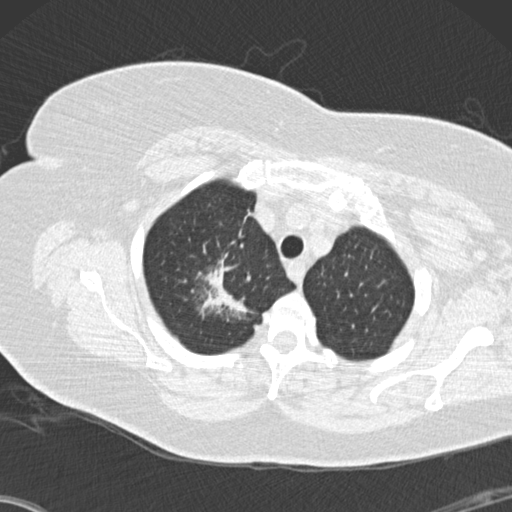
Low-dose screening chest CT, one axial slice. Slice 122 of 146 in the series (ordered by position). Reconstruction kernel B30f. Lung window (W 1500 / L -600 HU). 512 × 512 image matrix.
Annotated regions visible in this slice (manually delineated by an expert):
- lesion 1 (tumor, upper lobe of right lung): bounding box [x1, y1, x2, y2] px = [200, 255, 248, 316]